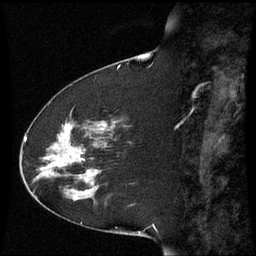
Breast MRI (dynamic contrast-enhanced), one sagittal slice; slice 19 of 60 in the series (ordered by position); dynamic contrast-enhanced series, image 2 of 3 at this slice position (ordered by acquisition); 1.5 T; TE 4.2 ms, TR 8.9 ms; 2.3 mm slice thickness; 256 × 256 image matrix, field of view 210 × 210 mm. Patient: female, 51 years. From the clinical record (not read from this slice): setting: breast cancer imaged before/during neoadjuvant chemotherapy; receptor status: HR-positive, HER2-negative.
Structures marked on this image (semi-automatically segmented with operator editing):
- analysis volume of interest (the breast-tissue region the enhancement analysis was run in; not a lesion): bounding box (x1, y1, x2, y2) in pixels: (50, 121, 117, 187)
- tumour enhancement mask (voxels above the 70 % enhancement threshold inside the analysis volume of interest): (58, 126, 88, 181)